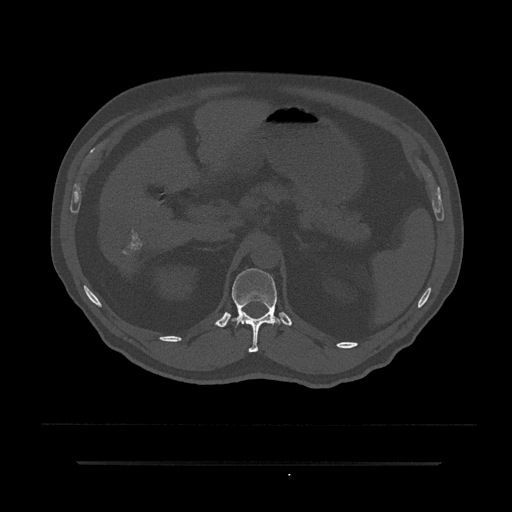
CT including the spine, one axial slice; position 207 of 797 along the scan axis; reconstruction kernel Br40s/3; 120 kVp; bone window (W 1800 / L 400 HU); 0.5 mm slice thickness; 512 × 512 image matrix, field of view 464 × 464 mm. Patient: male, 59 years. From the clinical record (not read from this slice): primary cancer: bile ducts.
Annotated regions visible in this slice (semi-automatic segmentation, software-assisted and operator-edited):
- T12 vertebra: bounding box <232,268,283,353> (left, top, right, bottom; pixels)